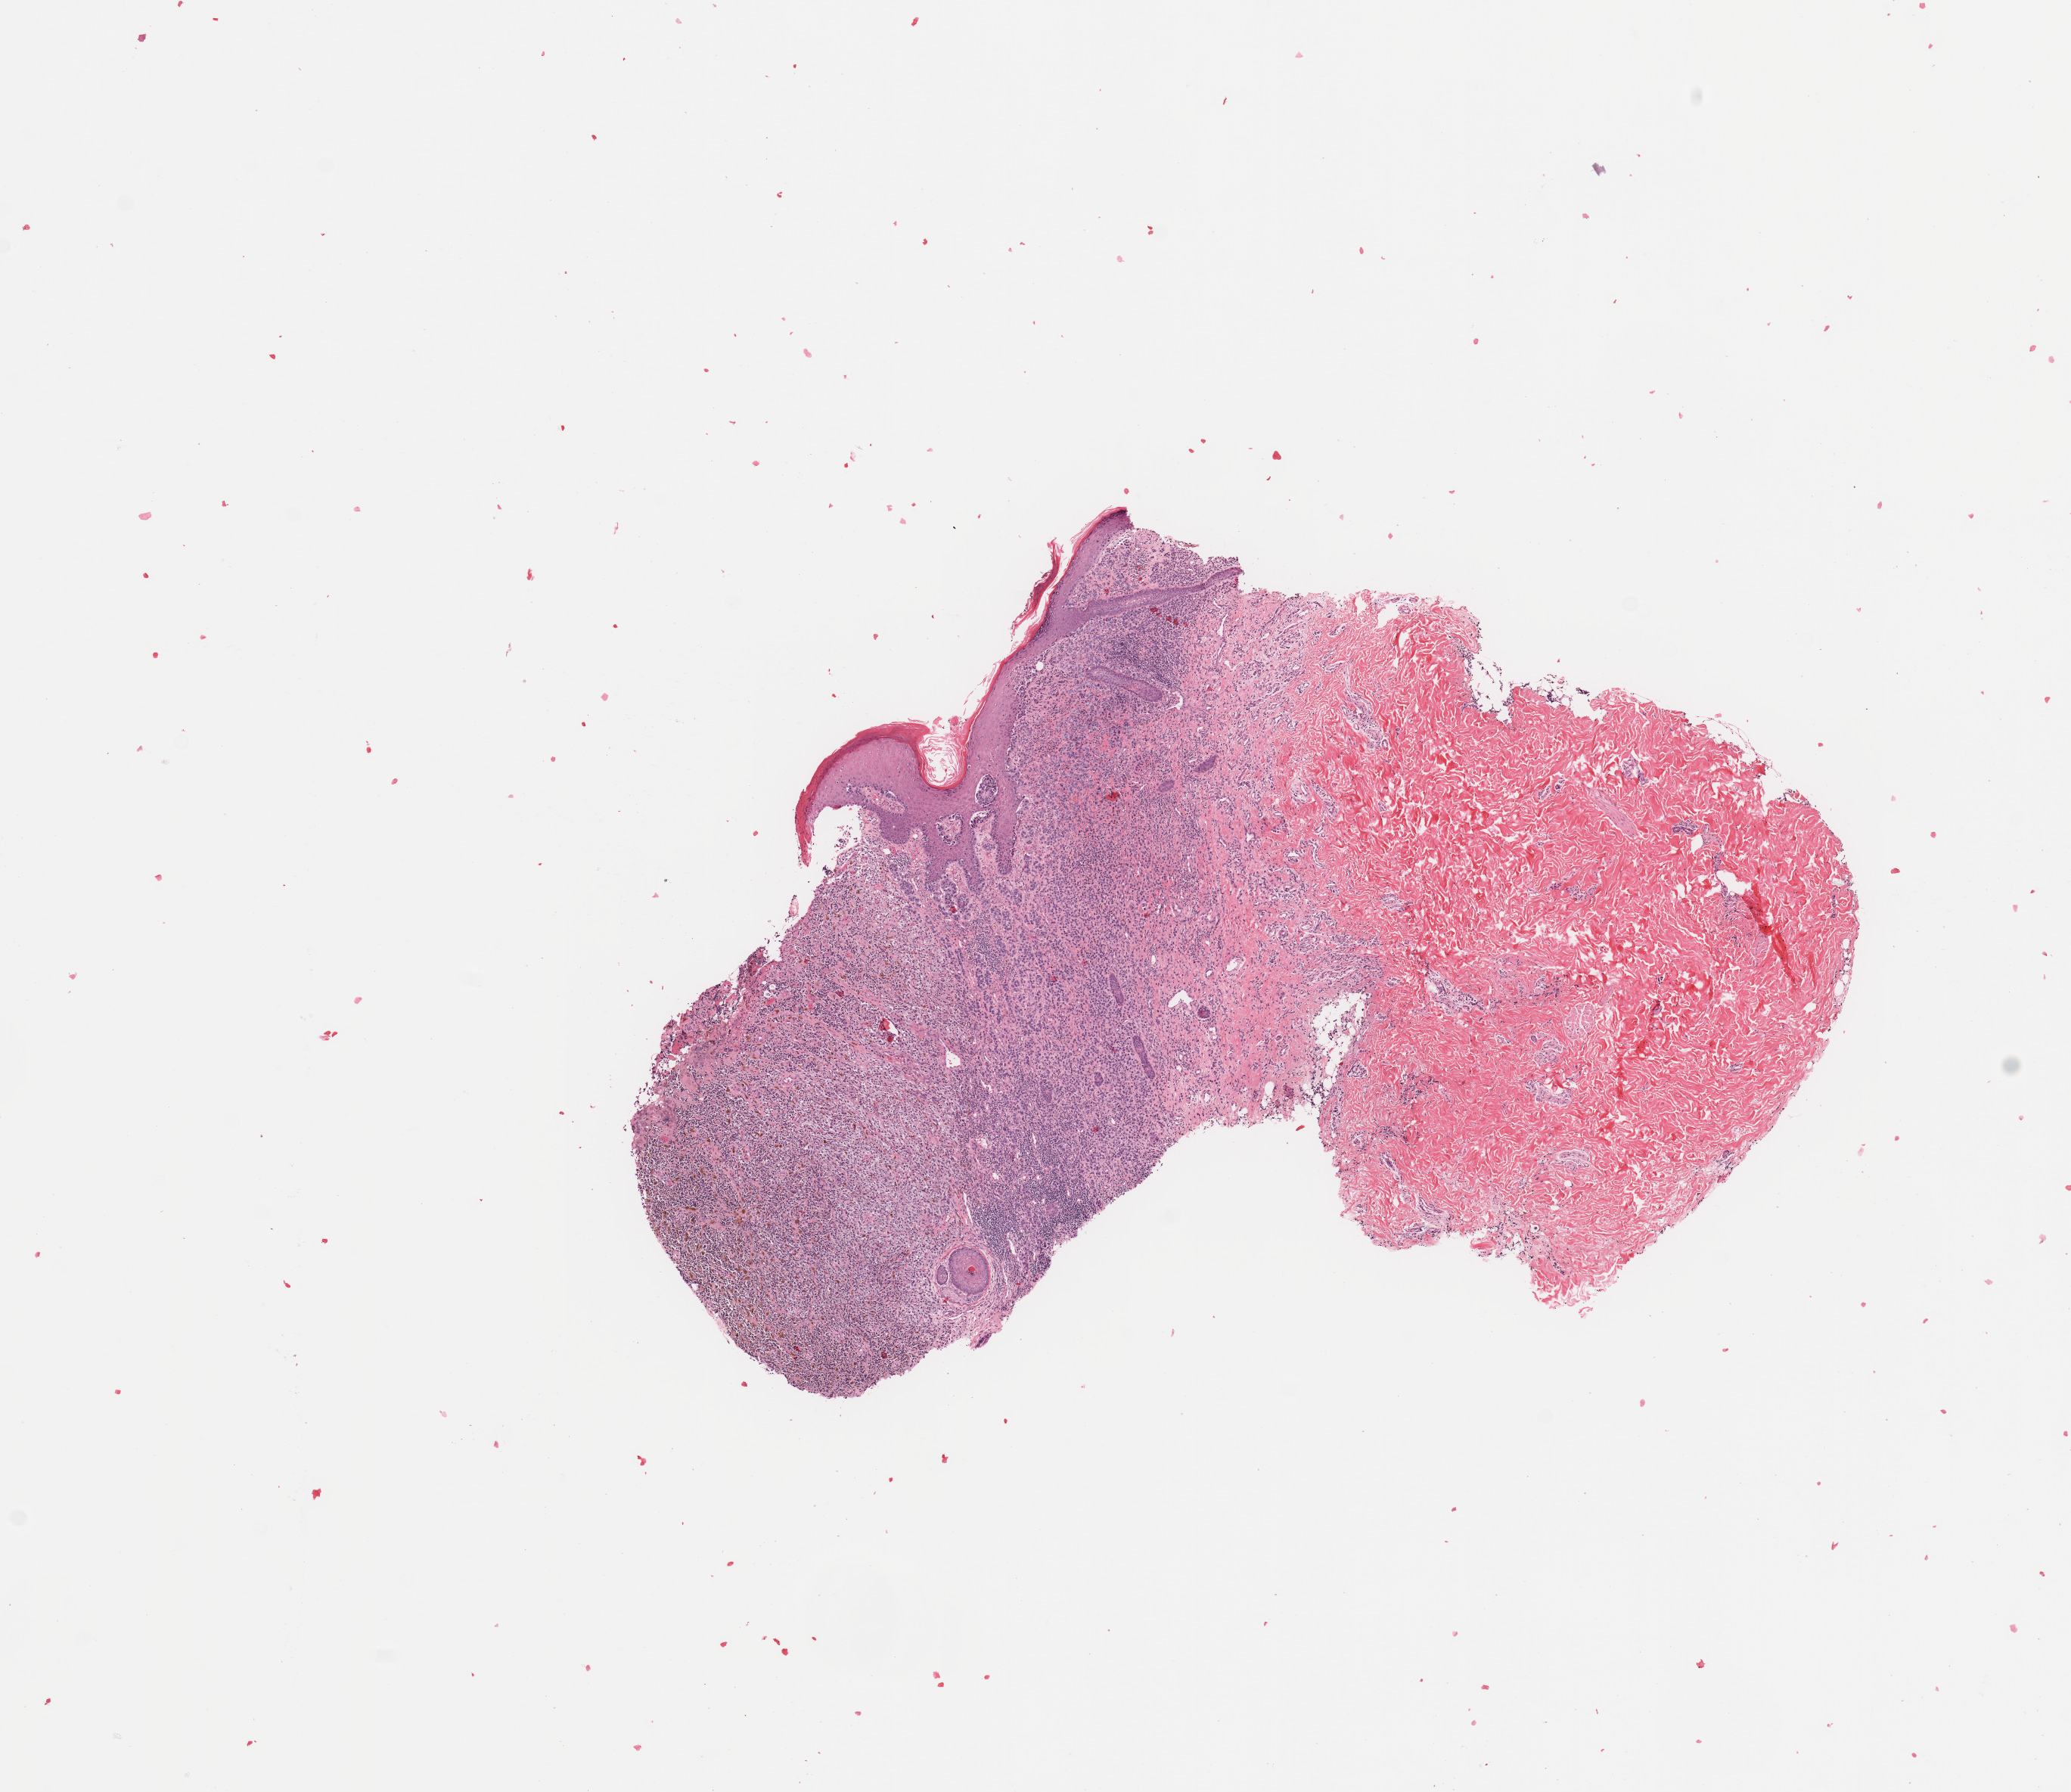
Digitized H&E-stained tissue section (whole slide) — a low-resolution overview of the entire scanned area, about 10.8 x 9.4 mm (acquisition: 20x scan). Tumour tissue sample, sampled site: skin. 49-year-old female patient. Pathologist review of this section (percent, as recorded): tumour nuclei 80%, necrosis 0%.
* histologic diagnosis: Malignant melanoma, NOS
* primary tumour site (as recorded): trunk